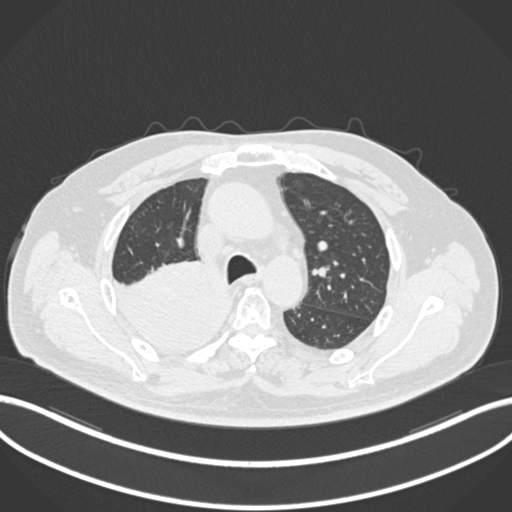
Chest CT, one axial slice; slice 142 of 218 in the series (ordered by position); reconstruction kernel B30f; 120 kVp; lung window (W 1500 / L -600 HU); 1 mm slice thickness; 512 × 512 image matrix, field of view 400 × 400 mm. Patient: male, 68 years. Case-level facts recorded for this patient, not image findings: clinical TNM (as recorded): T2a N0 M0.
Structures marked on this image (bounding box drawn by a radiologist):
- lung tumour (recorded histology: adenocarcinoma): box from (x=114, y=261) to (x=234, y=353) px